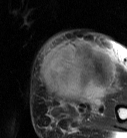
MRI of an extremity soft-tissue mass, one axial slice; T2-weighted fat-saturated; MR volume resampled by the dataset authors to the PET/CT grid (not the native acquisition matrix); 3.27 mm slice thickness; 127 × 138 image matrix, field of view 124 × 135 mm. Female patient. Case-level facts recorded for this patient, not image findings: histological type: pleiomorphic leiomyosarcoma; grade: high; site of the primary tumour: left biceps.
Annotated regions visible in this slice (expert contour drawn on MRI and transferred to this co-registered scan by the dataset authors):
- gross tumour volume including surrounding oedema: box from (x=40, y=39) to (x=117, y=106) px
- gross tumour volume (mass): (x=40, y=39)–(x=117, y=102)